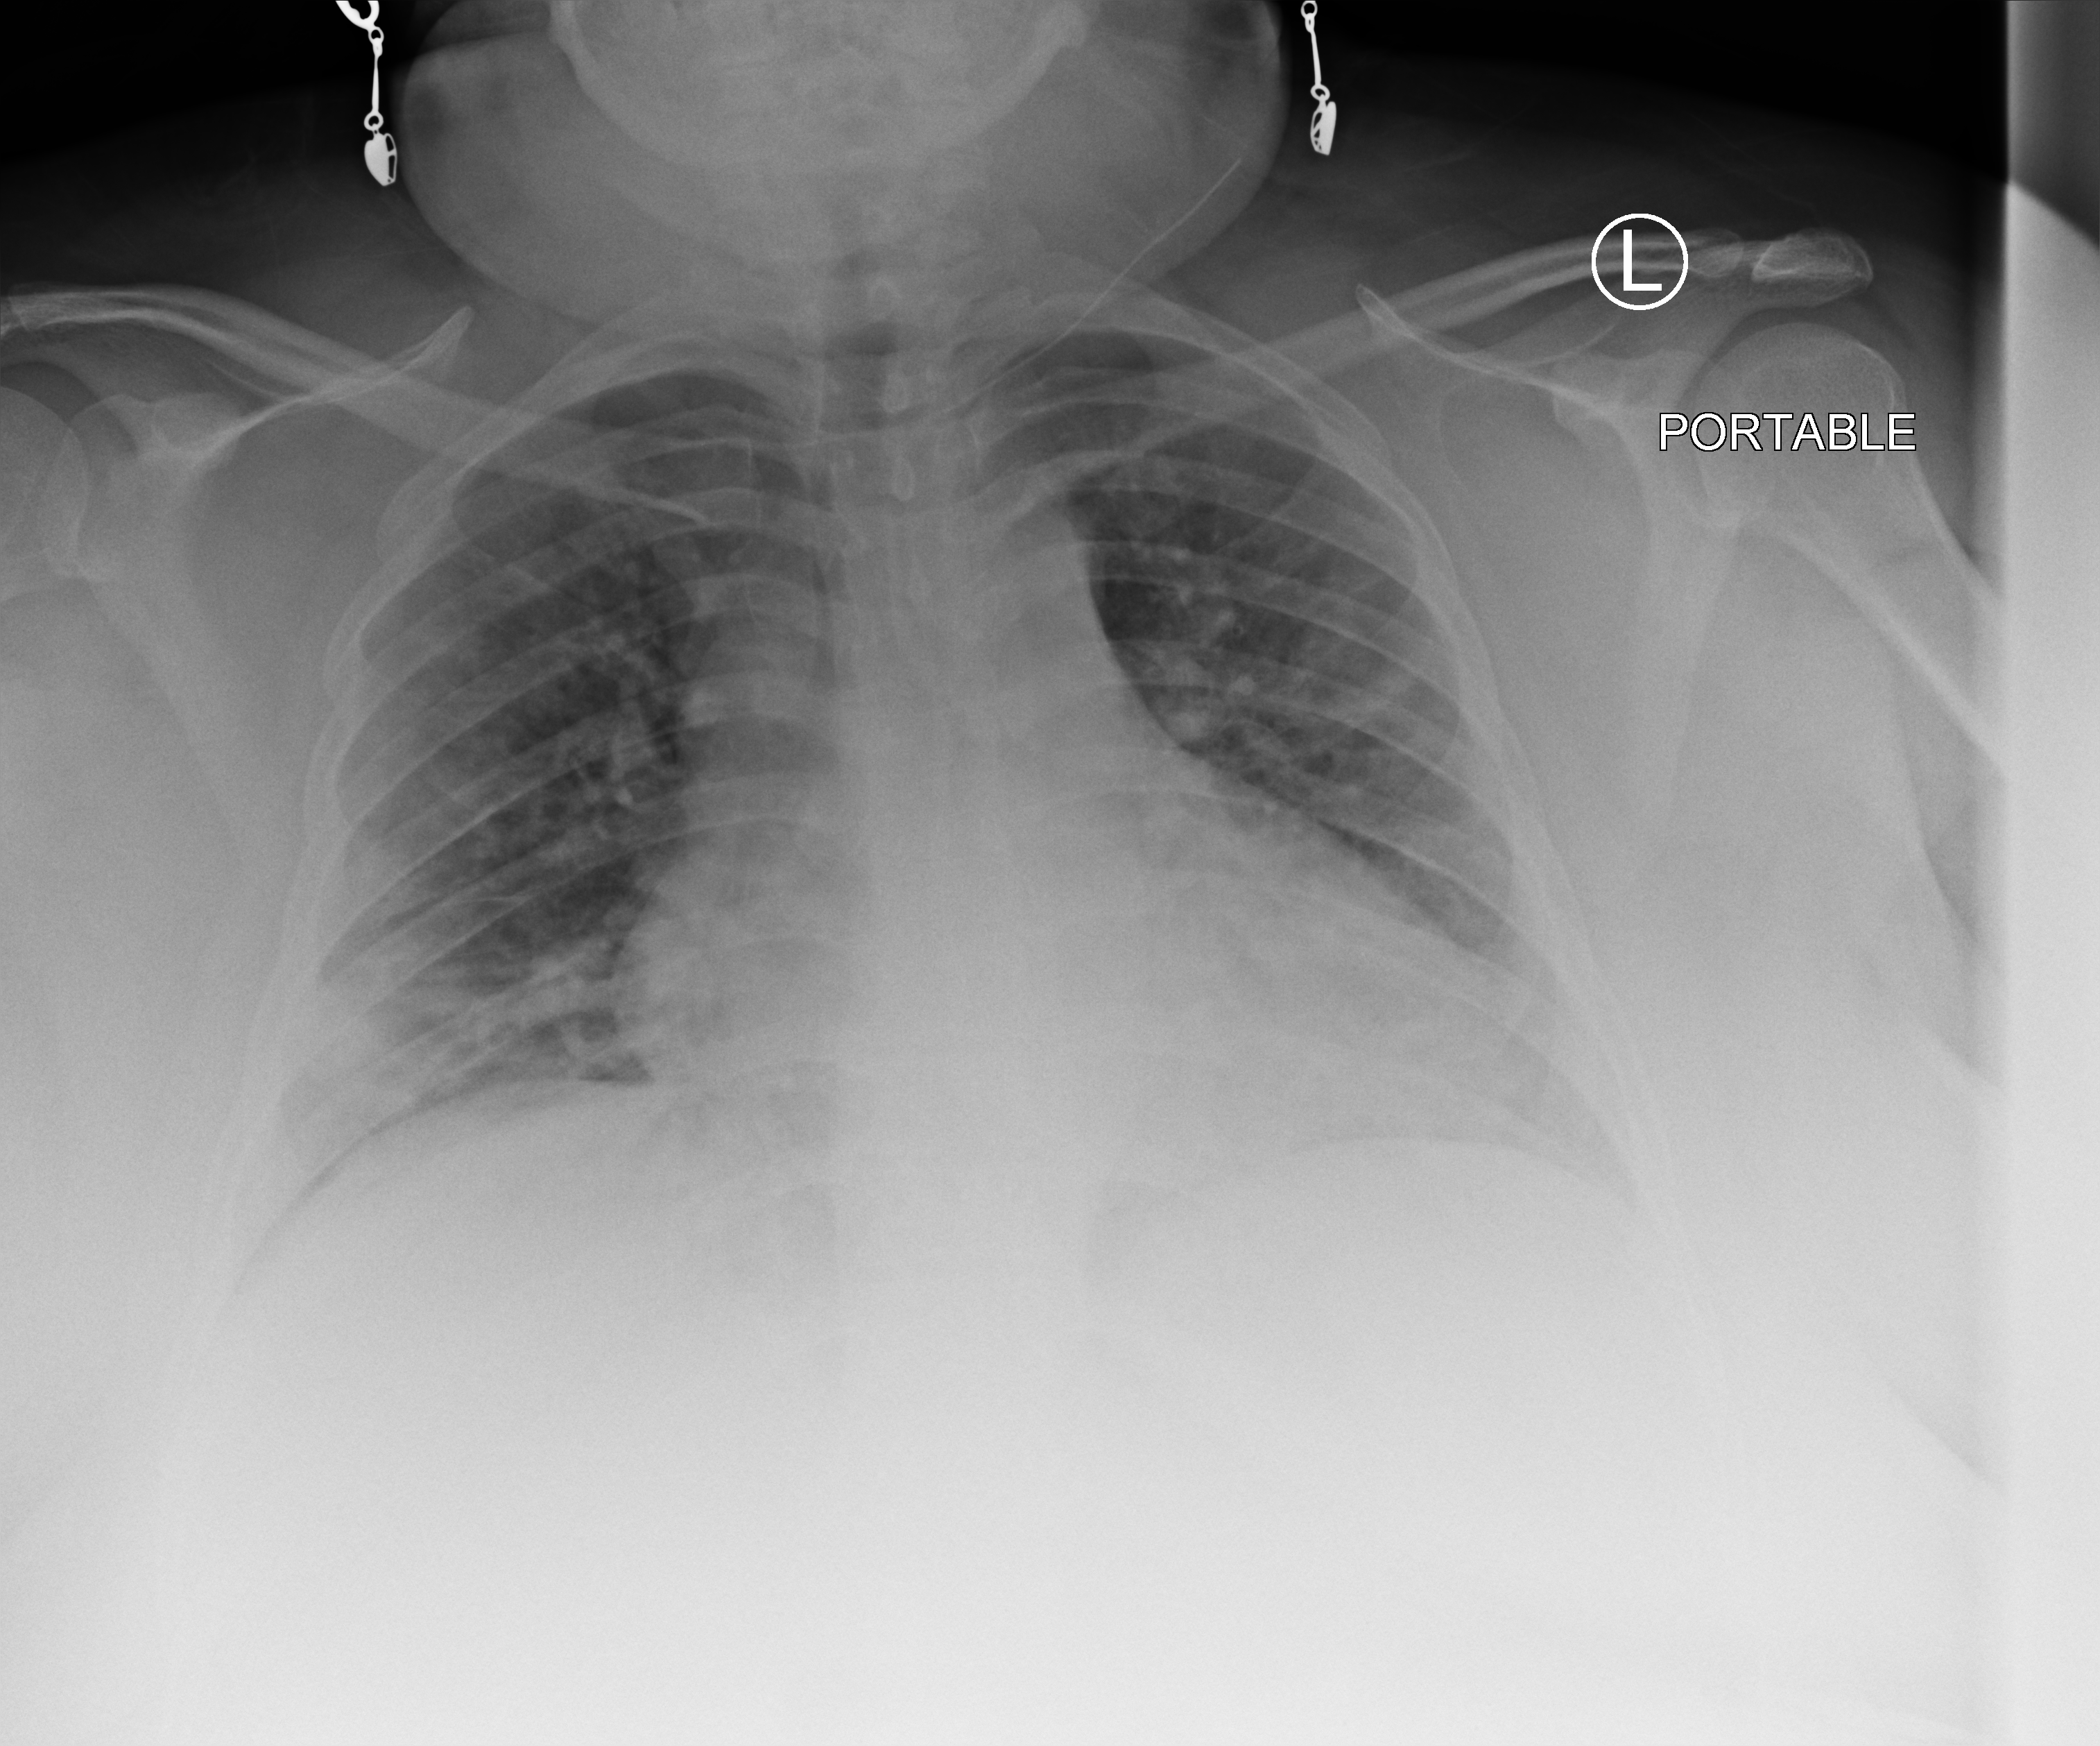
Chest X-ray (portable); anteroposterior (AP) projection. Patient hospitalised with COVID-19; female, aged 18–59 years.
Hospital-stay facts (about this admission, not read from this image; timing relative to this image not recorded):
- admitted to intensive care during this hospital stay: yes